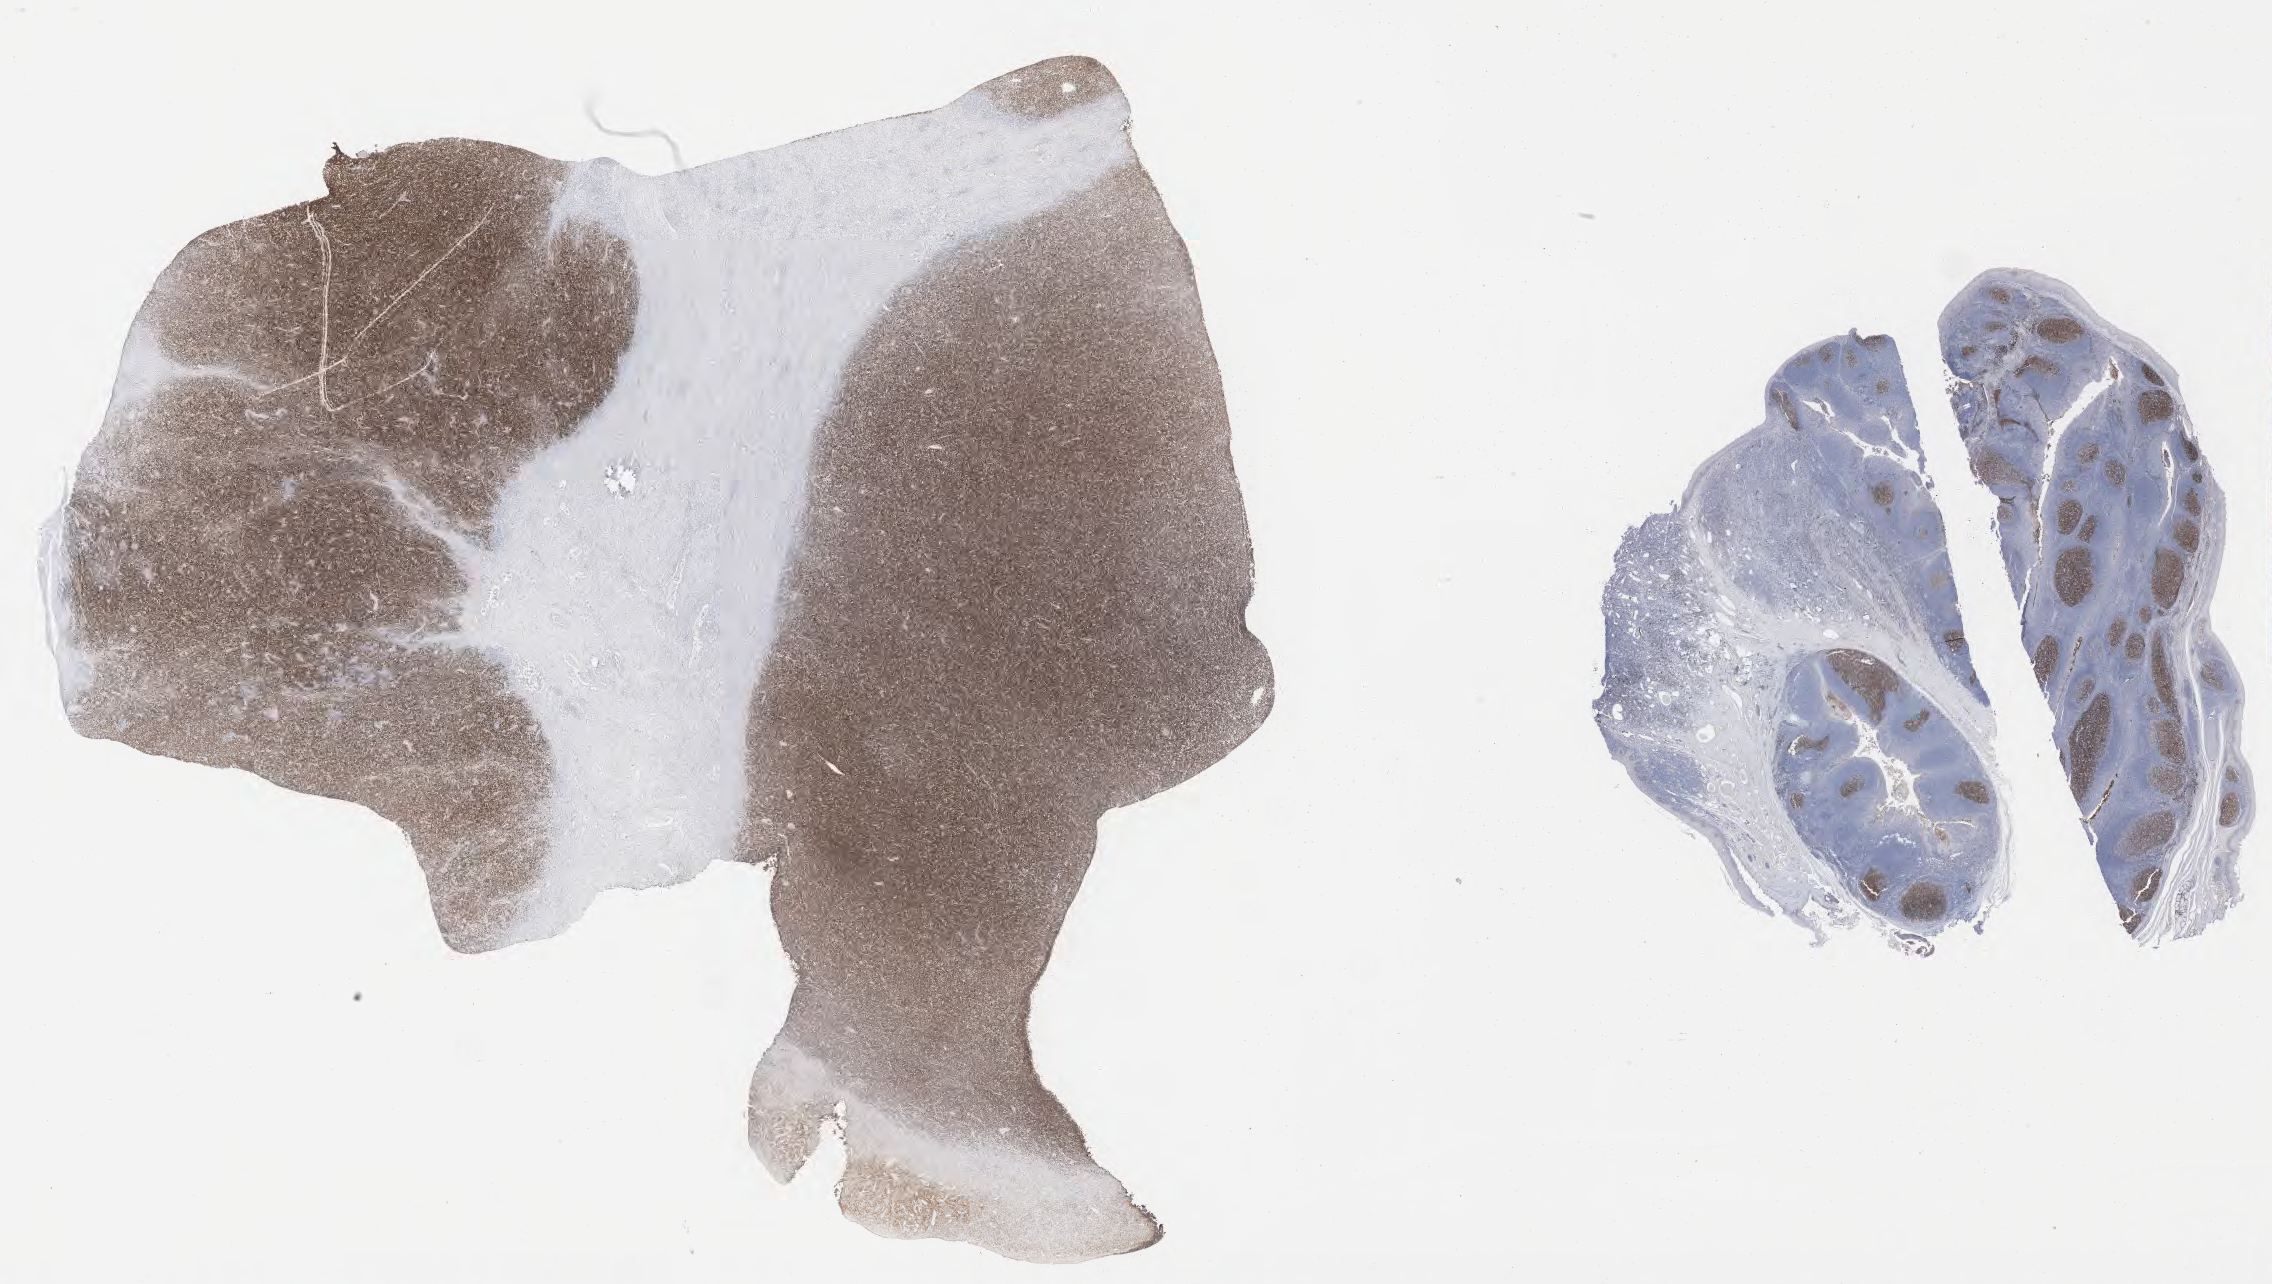
IHC for CD10, whole-slide image, a low-resolution overview of the entire scanned area, about 36.7 x 20.8 mm, tumor tissue. Female patient; age at initial diagnosis 8 years.
Histologic diagnosis: Burkitt lymphoma, NOS.